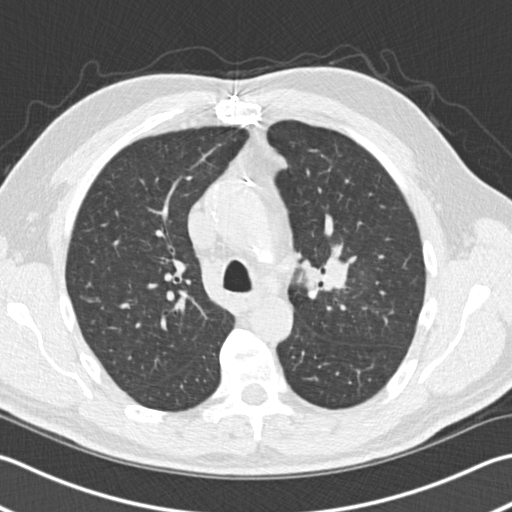
Low-dose screening chest CT, axial slice; third annual screen; lung window (W 1500 / L -600 HU); 2 mm slice thickness; 512 × 512 image matrix, field of view 346 × 346 mm. Male participant, aged 65 years at enrolment. Former smoker at enrolment.
• Lesion marked by an expert reader, bounding box (x1, y1, x2, y2) in pixels: (307, 239, 371, 303).
• The screening reader recorded 4 non-calcified nodules or masses ≥4 mm on this exam (left upper lobe, left upper lobe, left lower lobe, right middle lobe); which of them this box marks is not recorded.
• Official screen result: positive, other.
• Later outcome: lung cancer diagnosed 196 days after this screen — acinar cell carcinoma, left upper lobe, stage IA (AJCC 6th edition), 25 mm at pathology.